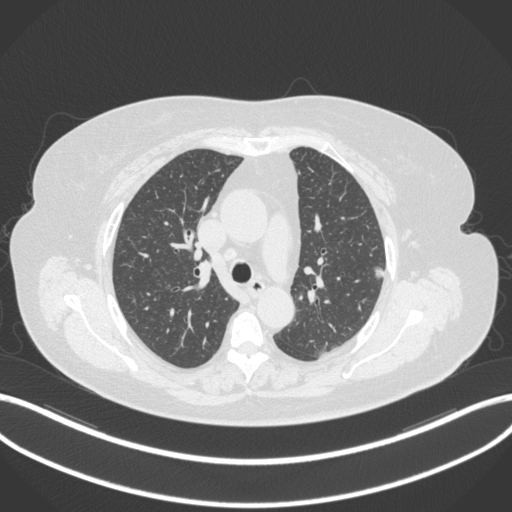
Chest CT, one axial slice. Position 219 of 310 along the scan axis. 120 kVp. Lung window (W 1500 / L -600 HU). 512 × 512 image matrix. Female patient, age 70 years. Case-level facts recorded for this patient, not image findings: clinical TNM (as recorded): T1c N0 M0.
Structures marked on this image (bounding box drawn by a radiologist):
- lung tumour (recorded histology: adenocarcinoma): bounding box [x1, y1, x2, y2] px = [371, 264, 383, 280]